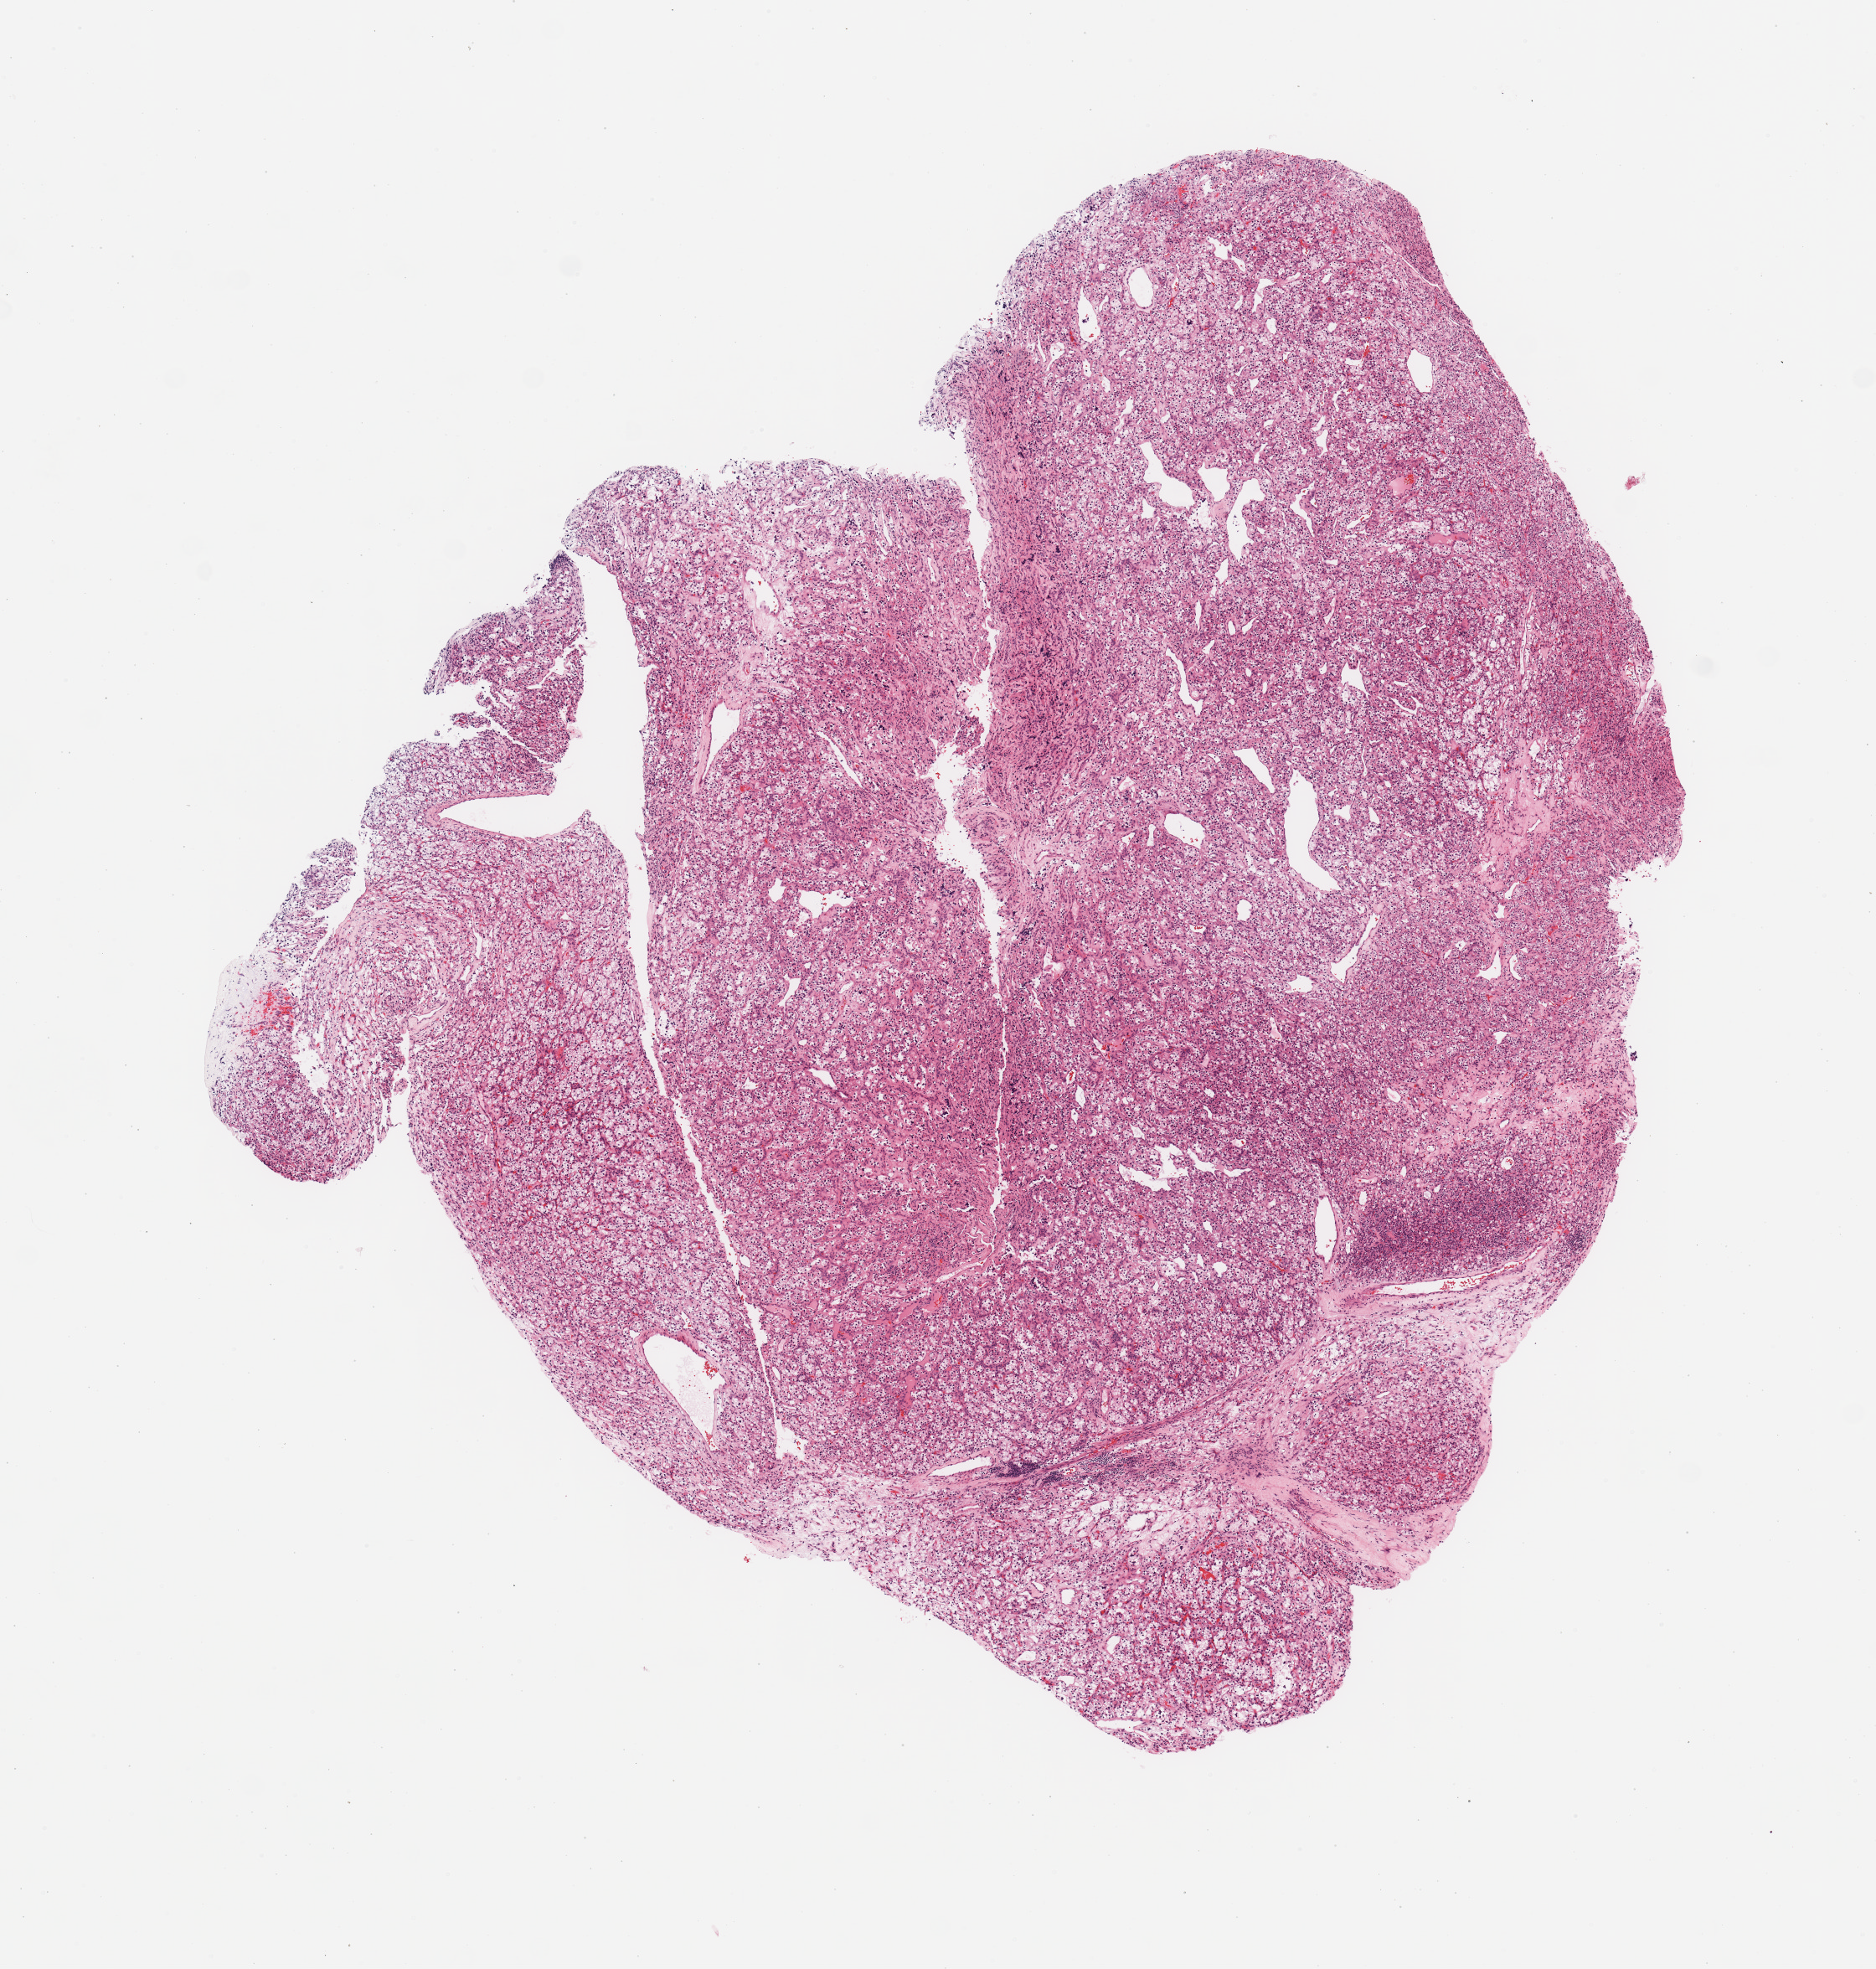
Whole-slide histology image, Hematoxylin and eosin (H&E) stained, whole scanned area (about 8.9 x 9.3 mm, acquisition: 20x scan) shown as a low-resolution overview; tumour tissue sample, sampled site: kidney. 66-year-old male patient. Histologic grade: G4 (undifferentiated). Slide review estimates, as recorded: tumour nuclei 95%, necrosis 2%.
AJCC pathologic stage: IV. Histologic diagnosis: Renal cell carcinoma, NOS. Primary tumour site (as recorded): lower pole.